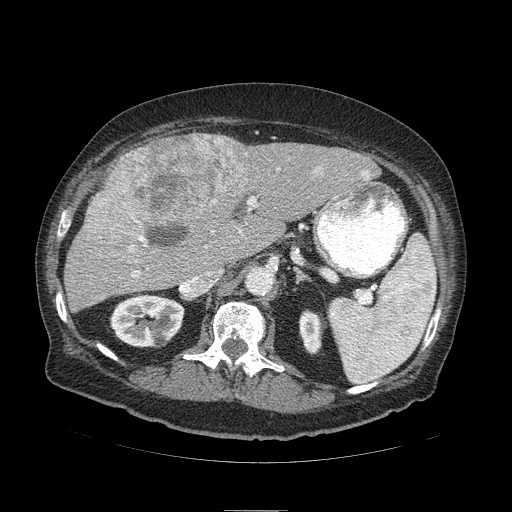
Contrast-enhanced abdominal CT (liver protocol), one axial slice; slice 55 of 103 in the series (ordered by position); reconstruction kernel STANDARD; 120 kVp; soft-tissue window (W 400 / L 40 HU); 512 × 512 image matrix, field of view 440 × 440 mm. Case-level facts recorded for this patient, not image findings: diagnosis: hepatocellular carcinoma (patient treated with transarterial chemoembolisation; whether this scan precedes or follows treatment is not stated here); TNM stage (as recorded): Stage-IIIA; Child-Pugh class: B; tumour differentiation: well differentiated; tumour nodularity: multinodular.
Structures marked on this image (semi-automatically segmented with operator editing):
- liver parenchyma outside the tumour (the mass and vessels are separate outlines, so this box may not span the whole liver): box from (x=64, y=134) to (x=378, y=310) px
- mass: (x=82, y=132)–(x=245, y=249)
- liver vessels: (x=129, y=171)–(x=369, y=277)